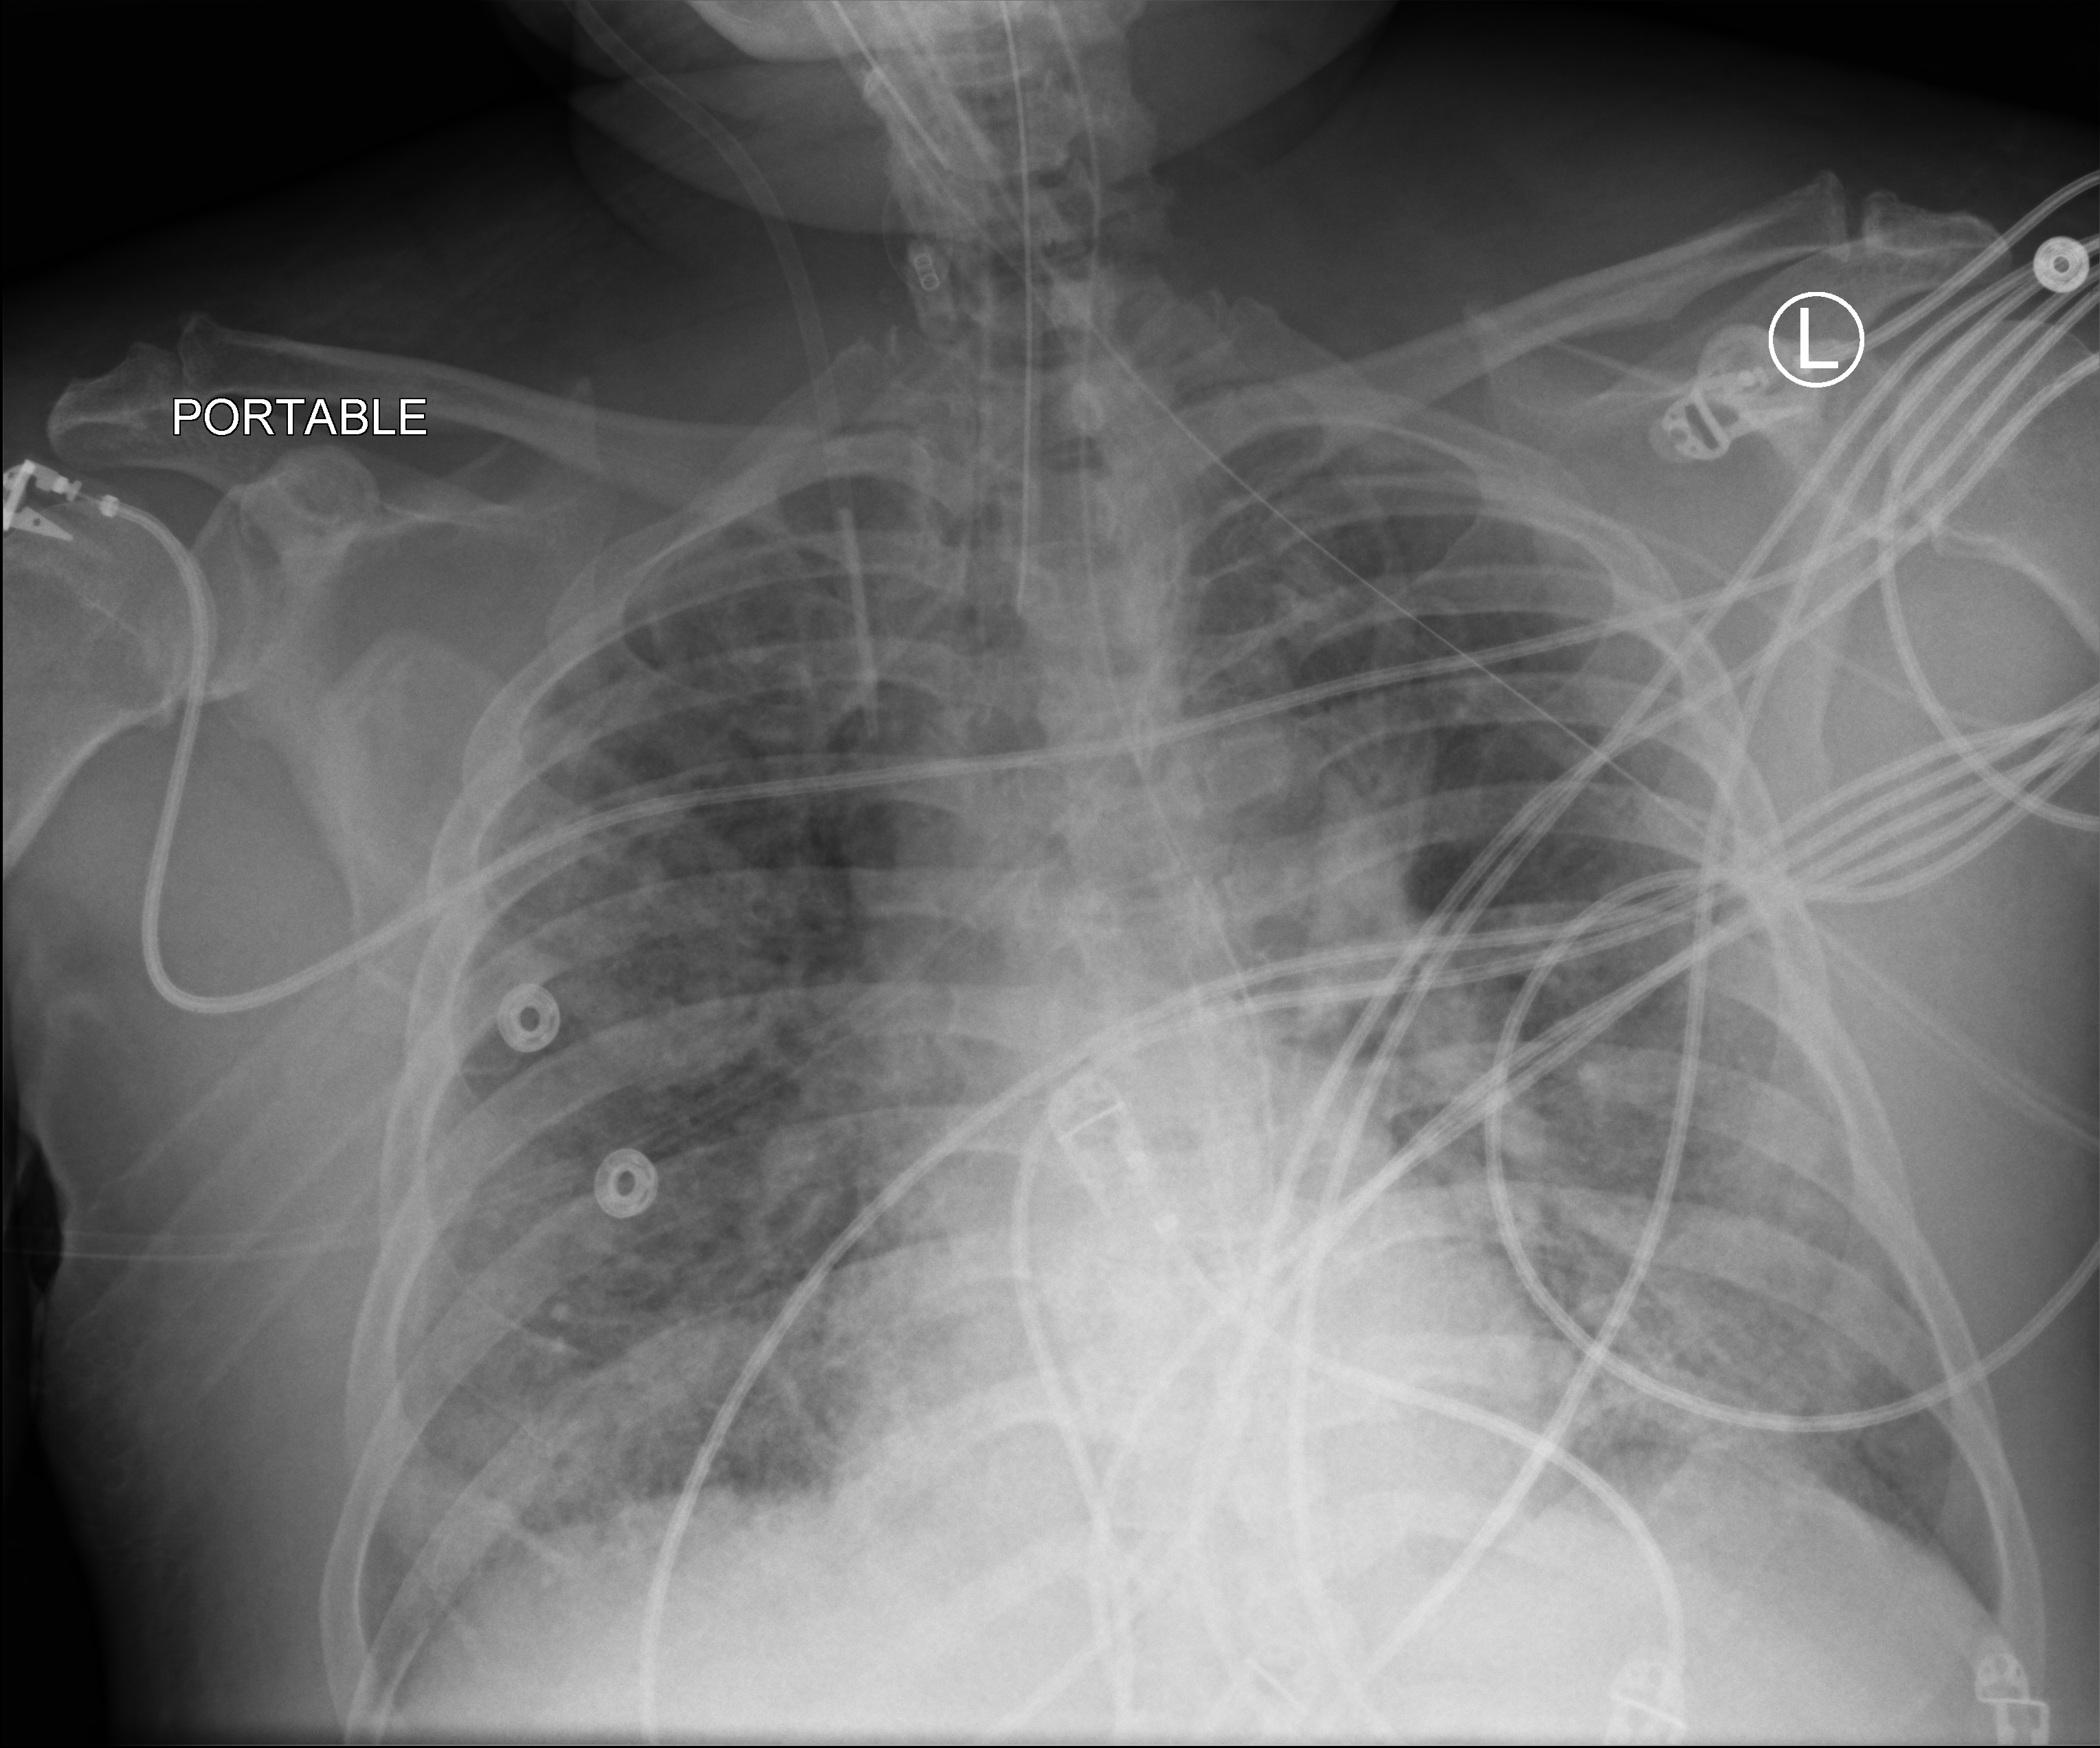
Chest X-ray (portable); anteroposterior (AP) projection. Patient hospitalised with COVID-19; male, aged 60–74 years.
Hospital-stay facts (about this admission, not read from this image; timing relative to this image not recorded): length of hospital stay: 28 days.